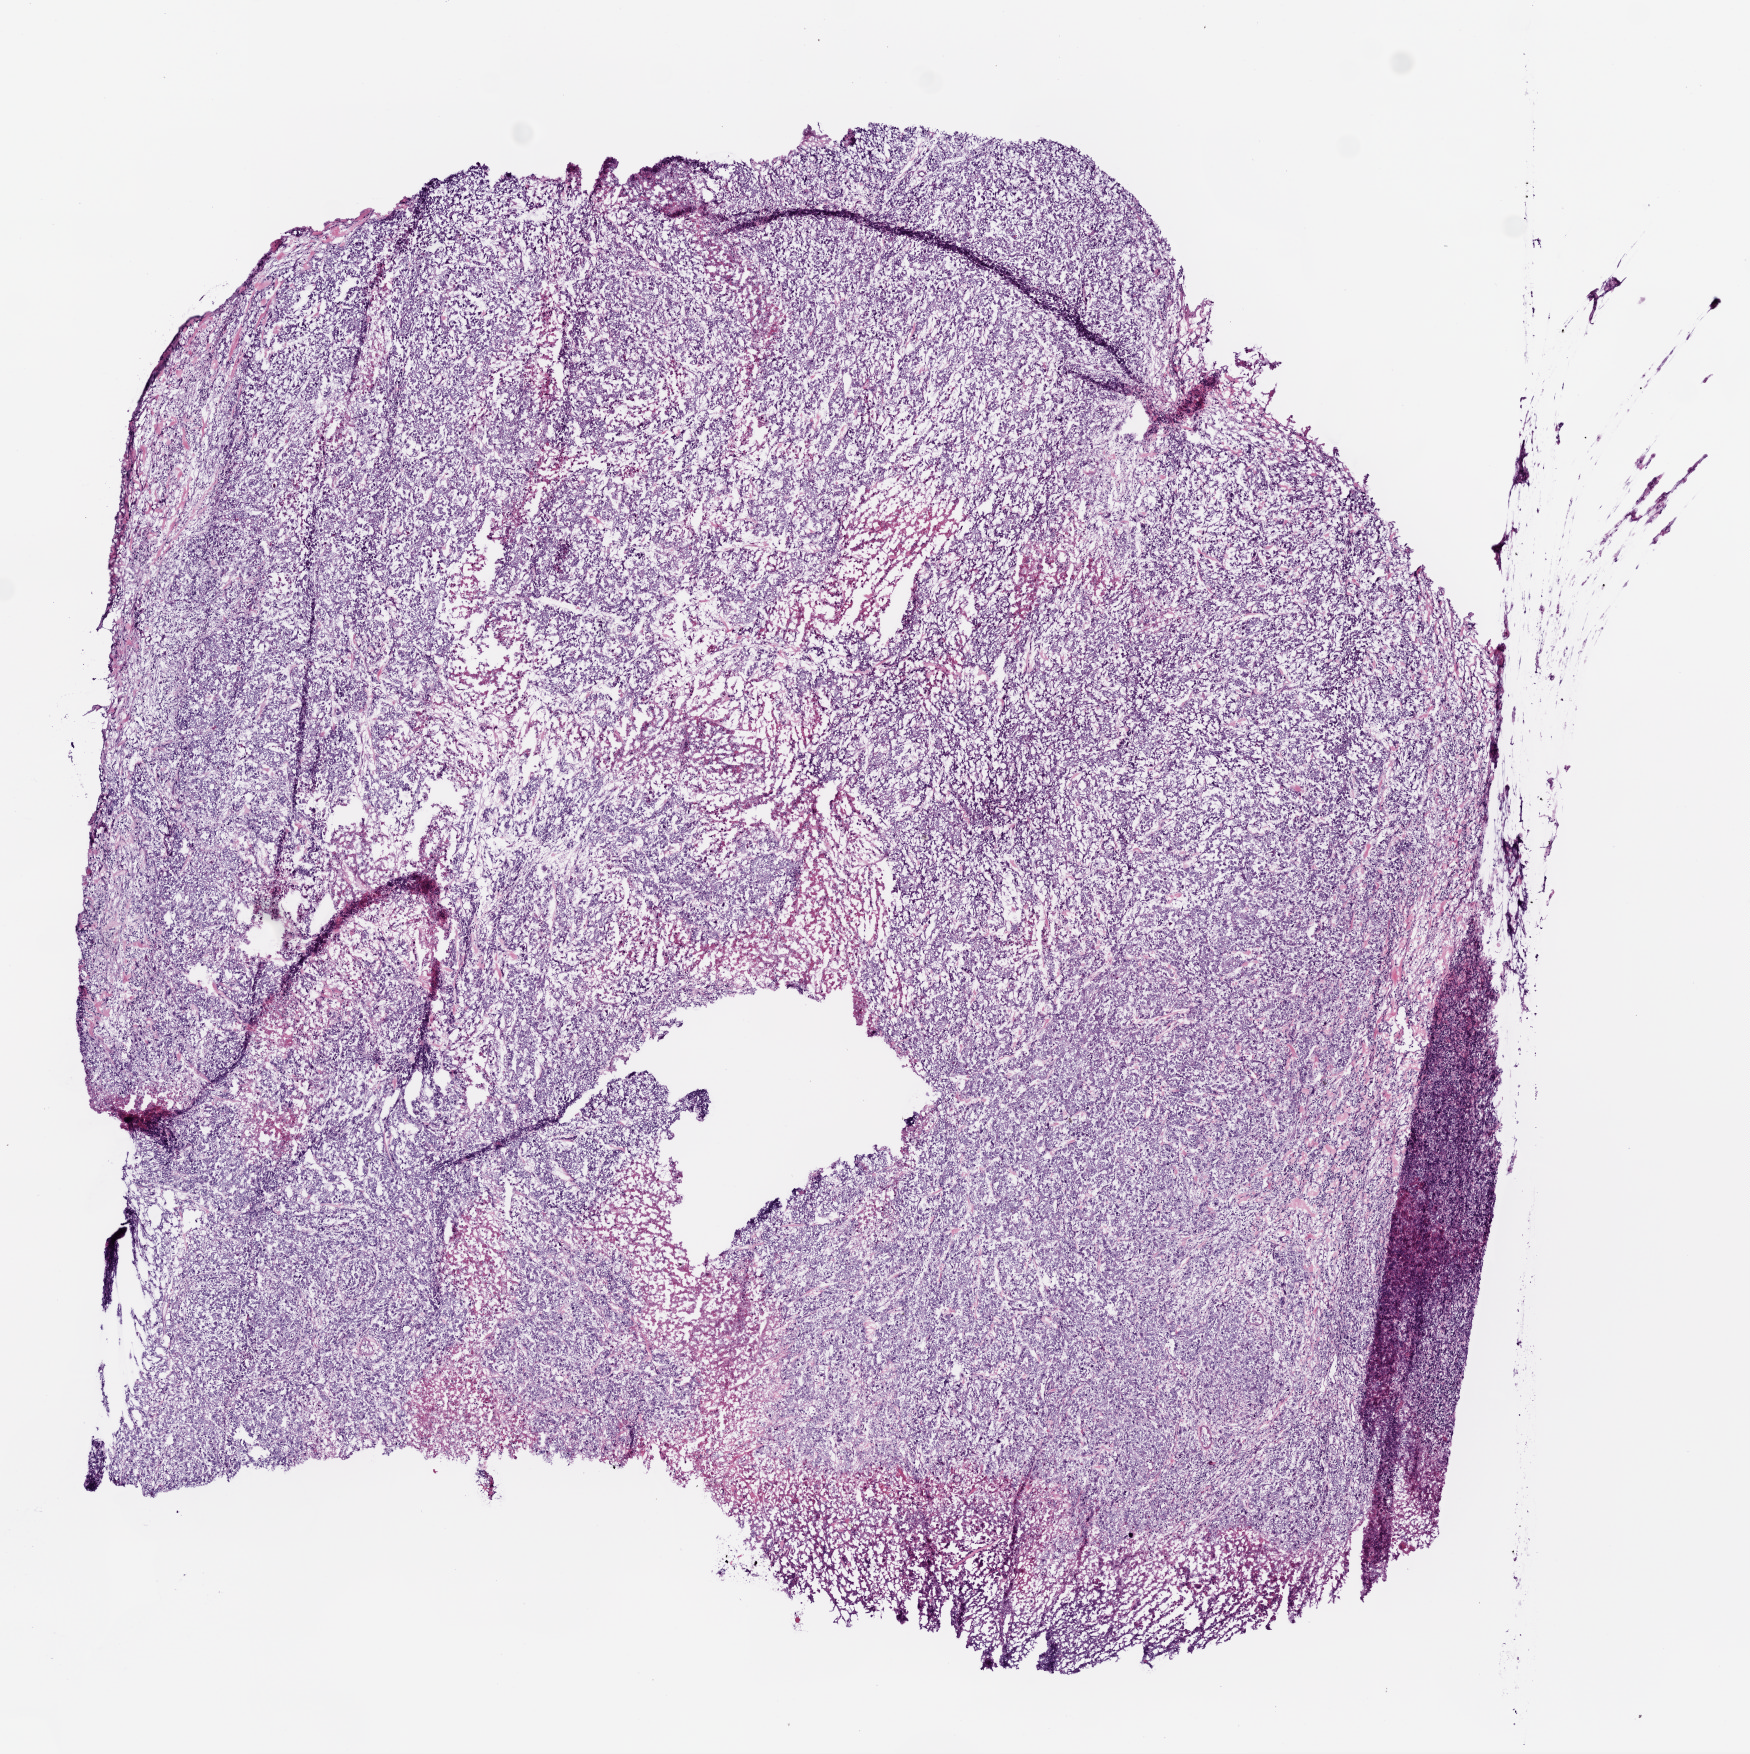
Hematoxylin and eosin (H&E) stained whole-slide image — whole scanned area (about 7.0 x 7.0 mm) shown as a low-resolution overview; frozen section; stomach, primary tumour sample. Female, age 68 years at initial diagnosis. Histologic grade: G3 (poorly differentiated). Pathologist review of this section (percent, as recorded): tumour cells 85%, tumour nuclei 80%, normal cells 0%, stromal cells 5%, necrosis 10%.
AJCC pathologic stage: IV (5th edition). Lymph nodes positive (case pathology): 18 of 24 examined. Pathologic diagnosis: Adenocarcinoma, intestinal type (body of stomach).